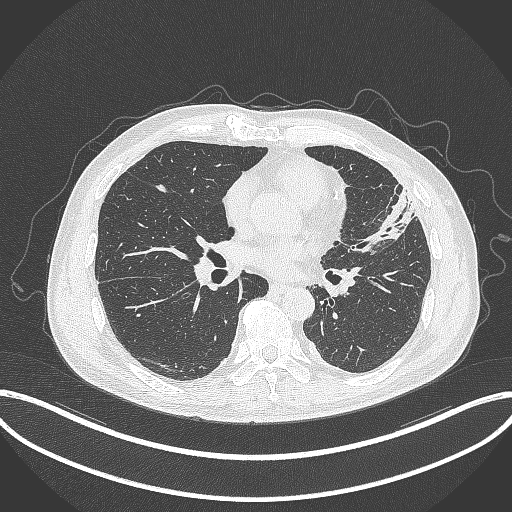
Chest CT, one axial slice. Slice 157 of 382 in the series (ordered by position). 120 kVp. Lung window (W 1500 / L -600 HU). 1 mm slice thickness. 512 × 512 image matrix, field of view 415 × 415 mm. Patient: male, 64 years. From the clinical record (not read from this slice): clinical TNM (as recorded): T4 N1 M0; histopathological grade: G3.
Structures marked on this image (bounding box drawn by a radiologist):
- lung tumour (recorded histology: adenocarcinoma): bounding box [x1, y1, x2, y2] px = [356, 184, 421, 246]